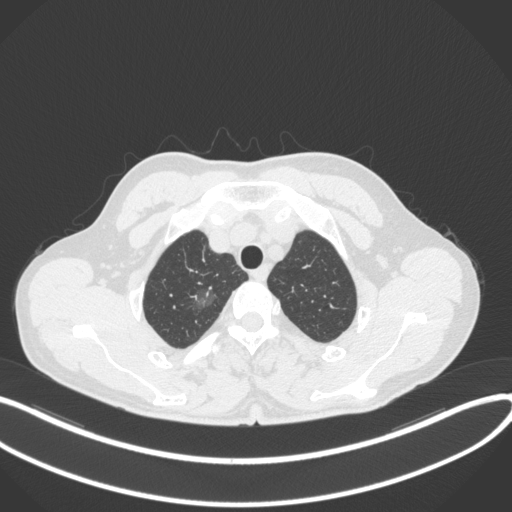
Chest CT, one axial slice; position 327 of 407 along the scan axis; 120 kVp; lung window (W 1500 / L -600 HU); 1 mm slice thickness; 512 × 512 image matrix, field of view 400 × 400 mm. Patient: male, 58 years. Case-level facts recorded for this patient, not image findings: clinical TNM (as recorded): T1c N0 M0; histopathological grade: G1-2.
Structures marked on this image (rectangle marked by the reading radiologist):
- lung tumour (recorded histology: adenocarcinoma): bounding box (x1, y1, x2, y2) in pixels: (186, 280, 222, 315)